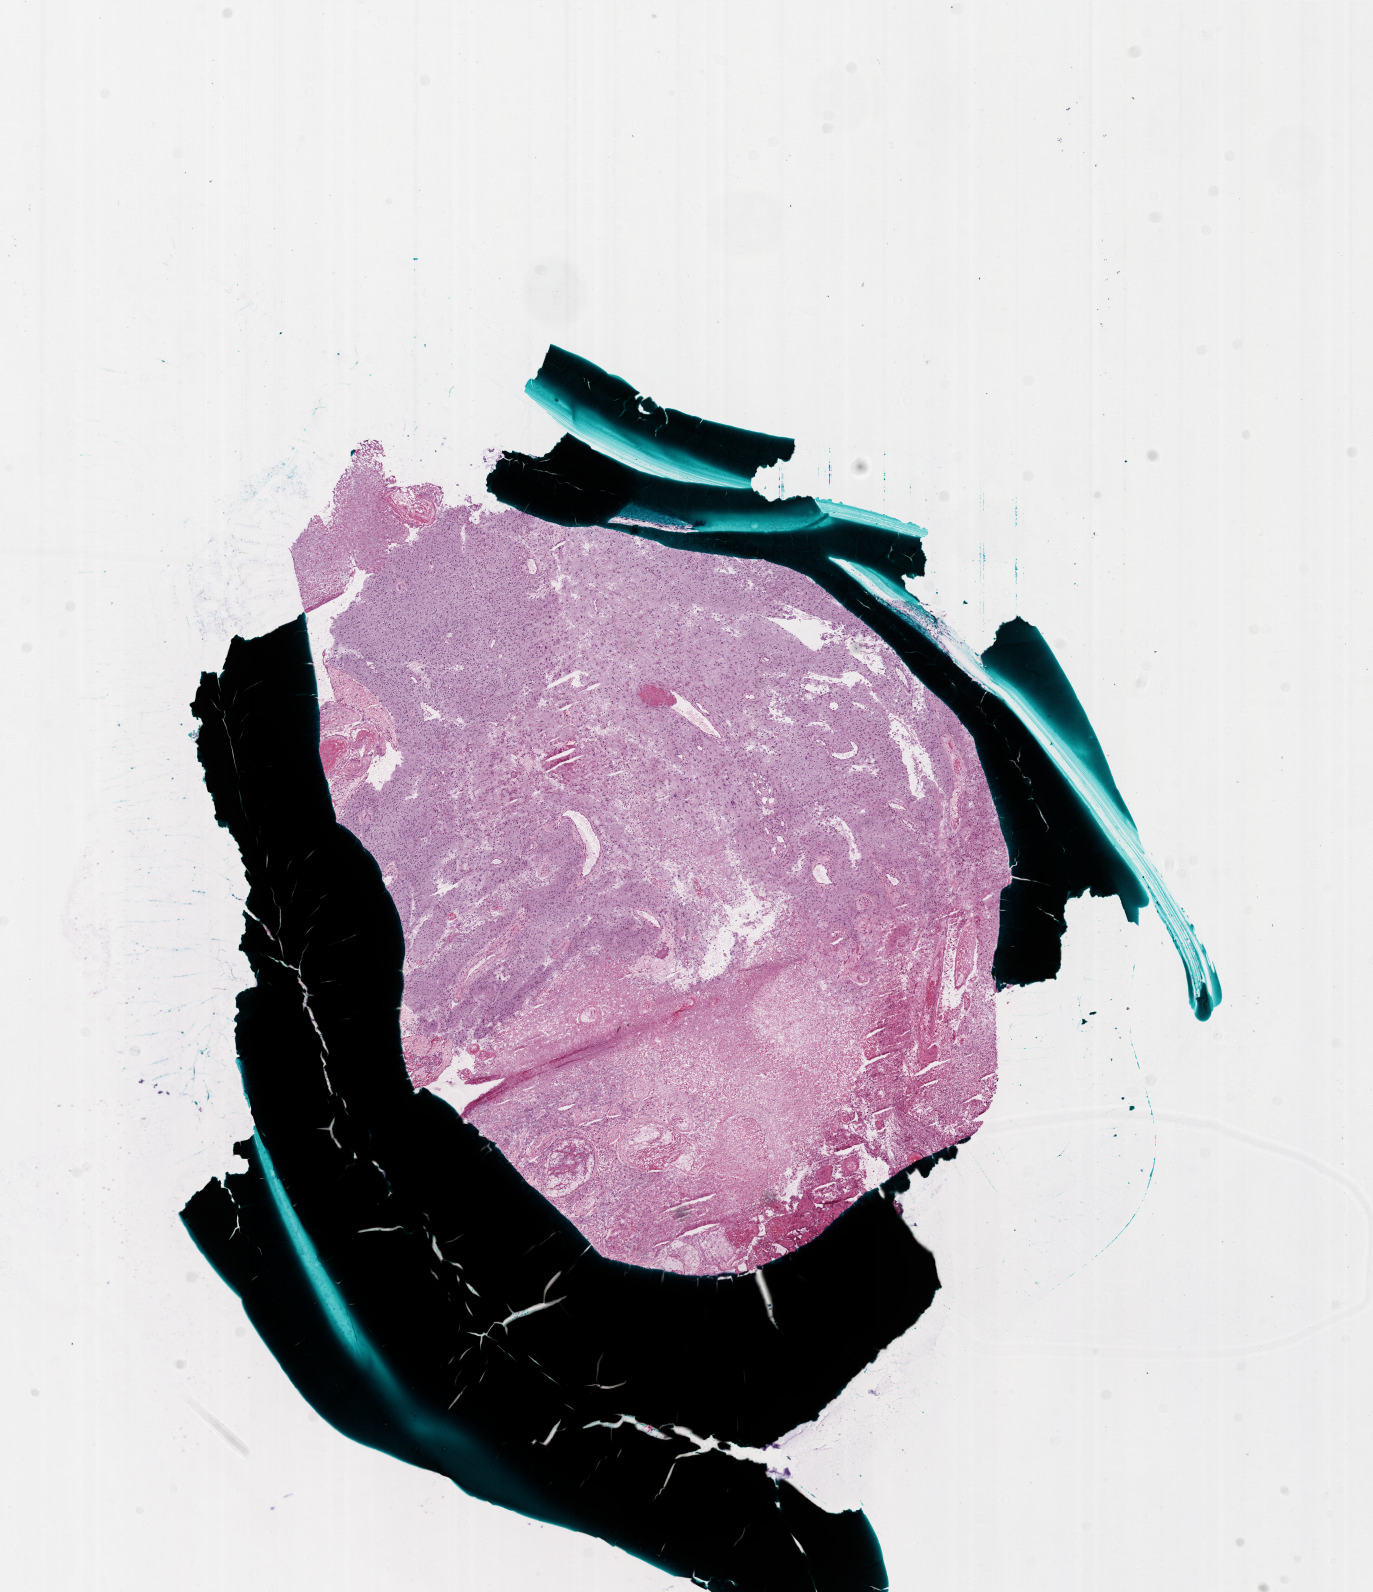
H&E-stained whole-slide image — a low-resolution overview of the entire scanned area, about 11.0 x 12.7 mm (from a 20x scan). Frozen section from the bottom of the tissue portion. Primary tumour sample from the brain. Male, age 55 years at initial diagnosis. Composition of this section per pathologist review: tumour cells 60%, tumour nuclei 100%, normal cells 0%, stromal cells 0%, necrosis 40%.
• histologic diagnosis: Glioblastoma